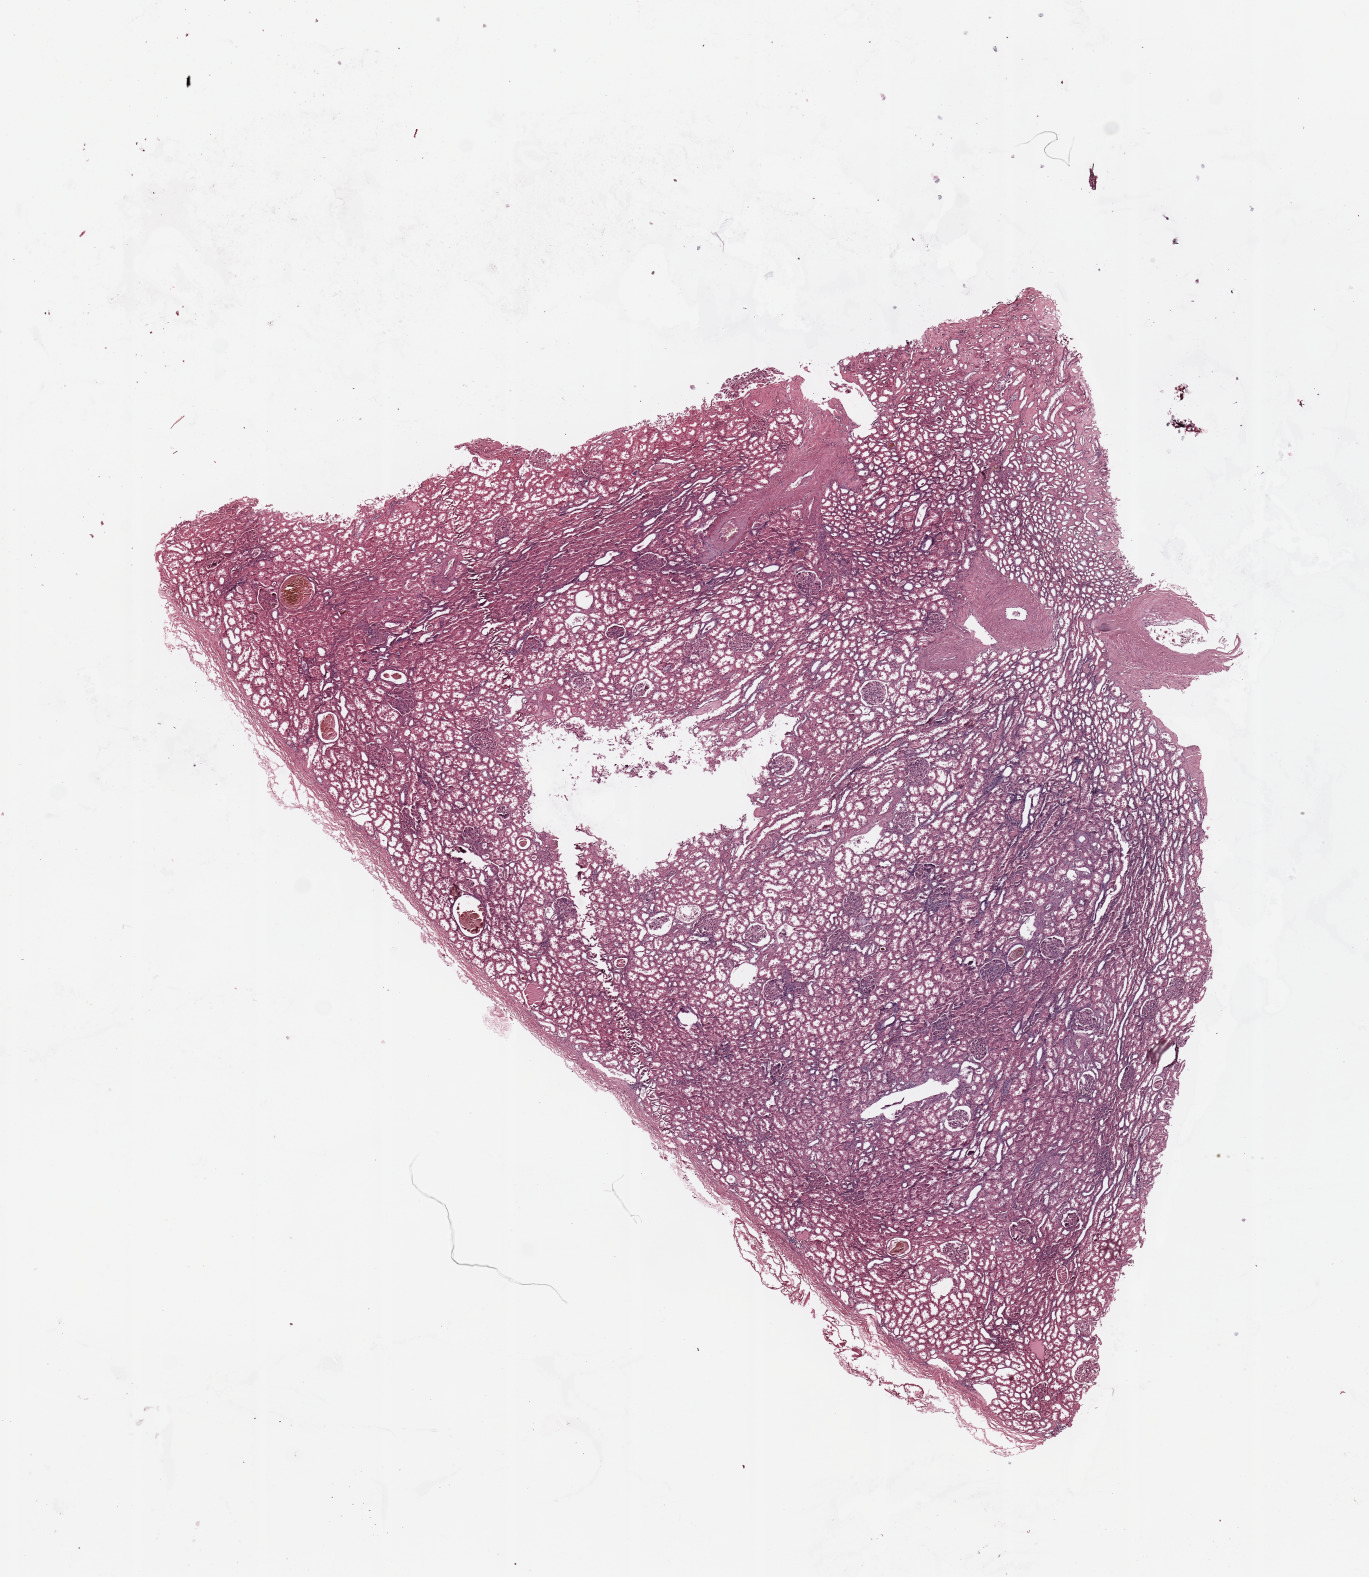
H&E-stained whole-slide image, low-resolution overview of the scanned area, about 10.8 x 12.5 mm (from a 20x scan), normal (non-tumour) tissue sample, sampled site: kidney. Patient: male, age 80 years.
This section: normal (non-tumour) tissue from the same patient. Patient diagnosis: Renal cell carcinoma, NOS.